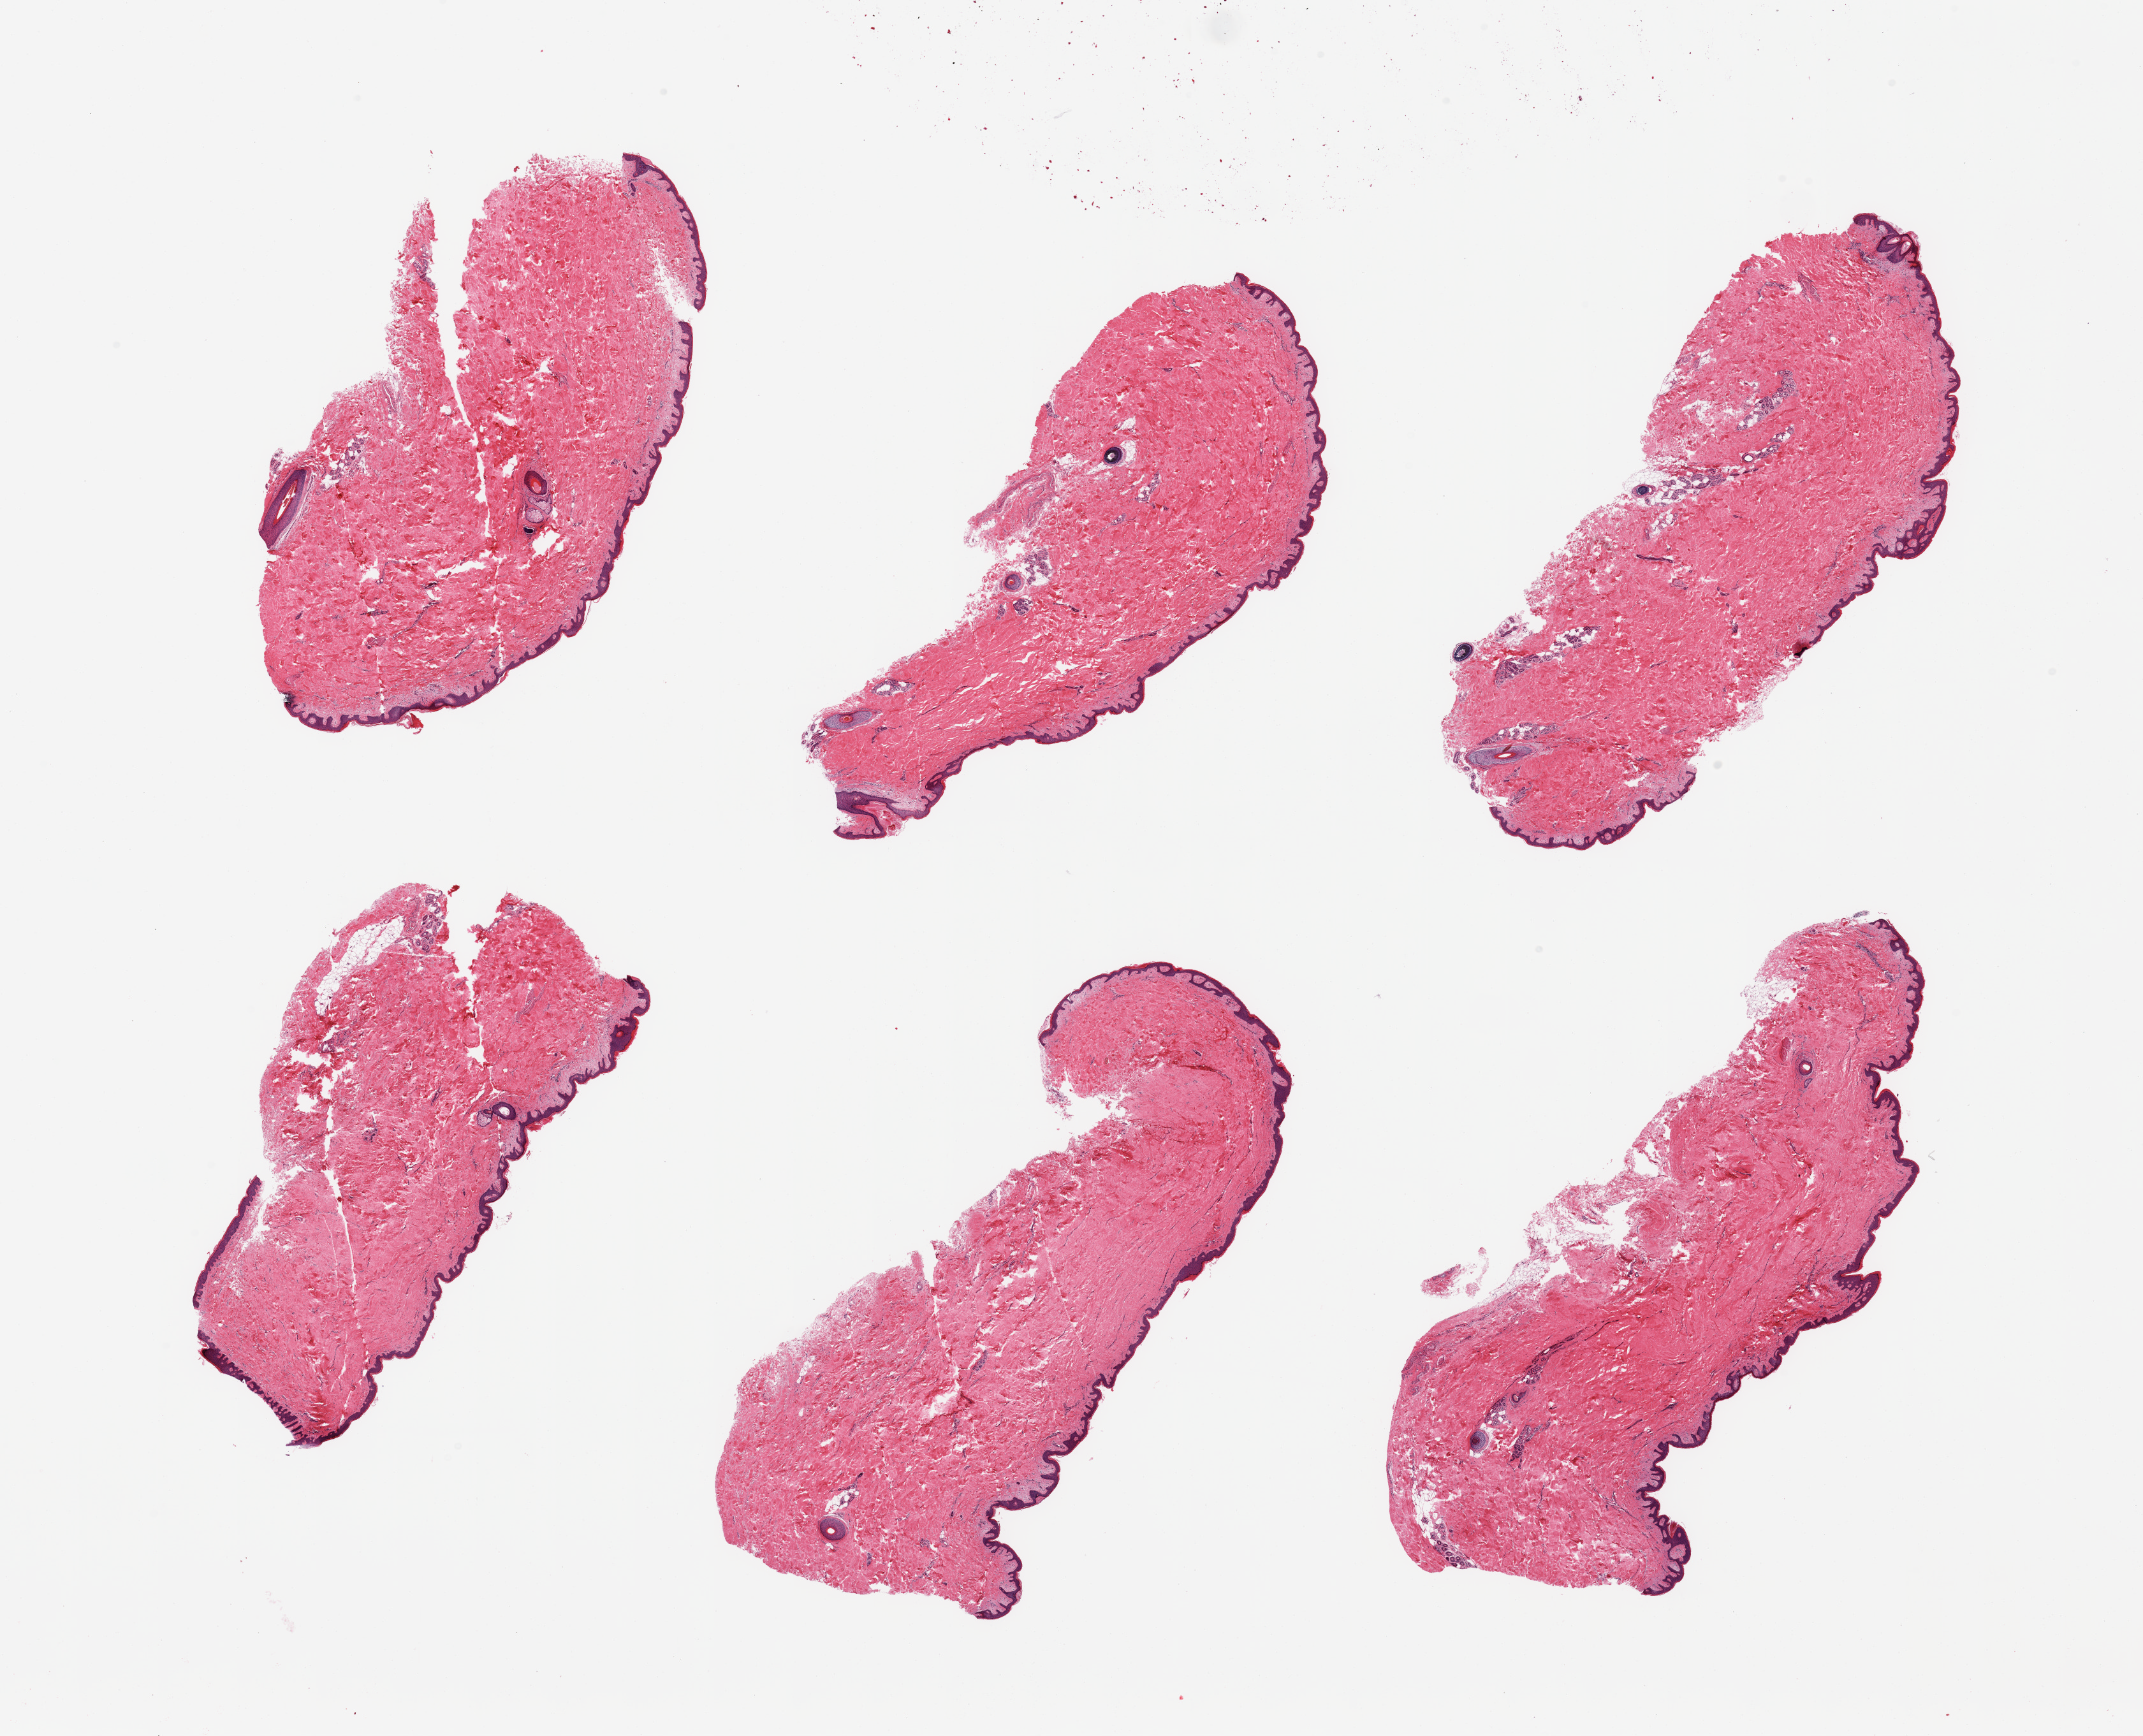
Hematoxylin and eosin (H&E) whole-slide image, whole scanned area (about 26.6 x 21.5 mm) shown as a low-resolution overview, PAXgene-fixed paraffin-embedded (PFPE) section, section of skin of suprapubic region (target tissue), donor tissue sample. Male donor.
- reviewer comment on this tissue sample: 6 pieces, no dermal fat; squamous epithelium is ~50-60 microns